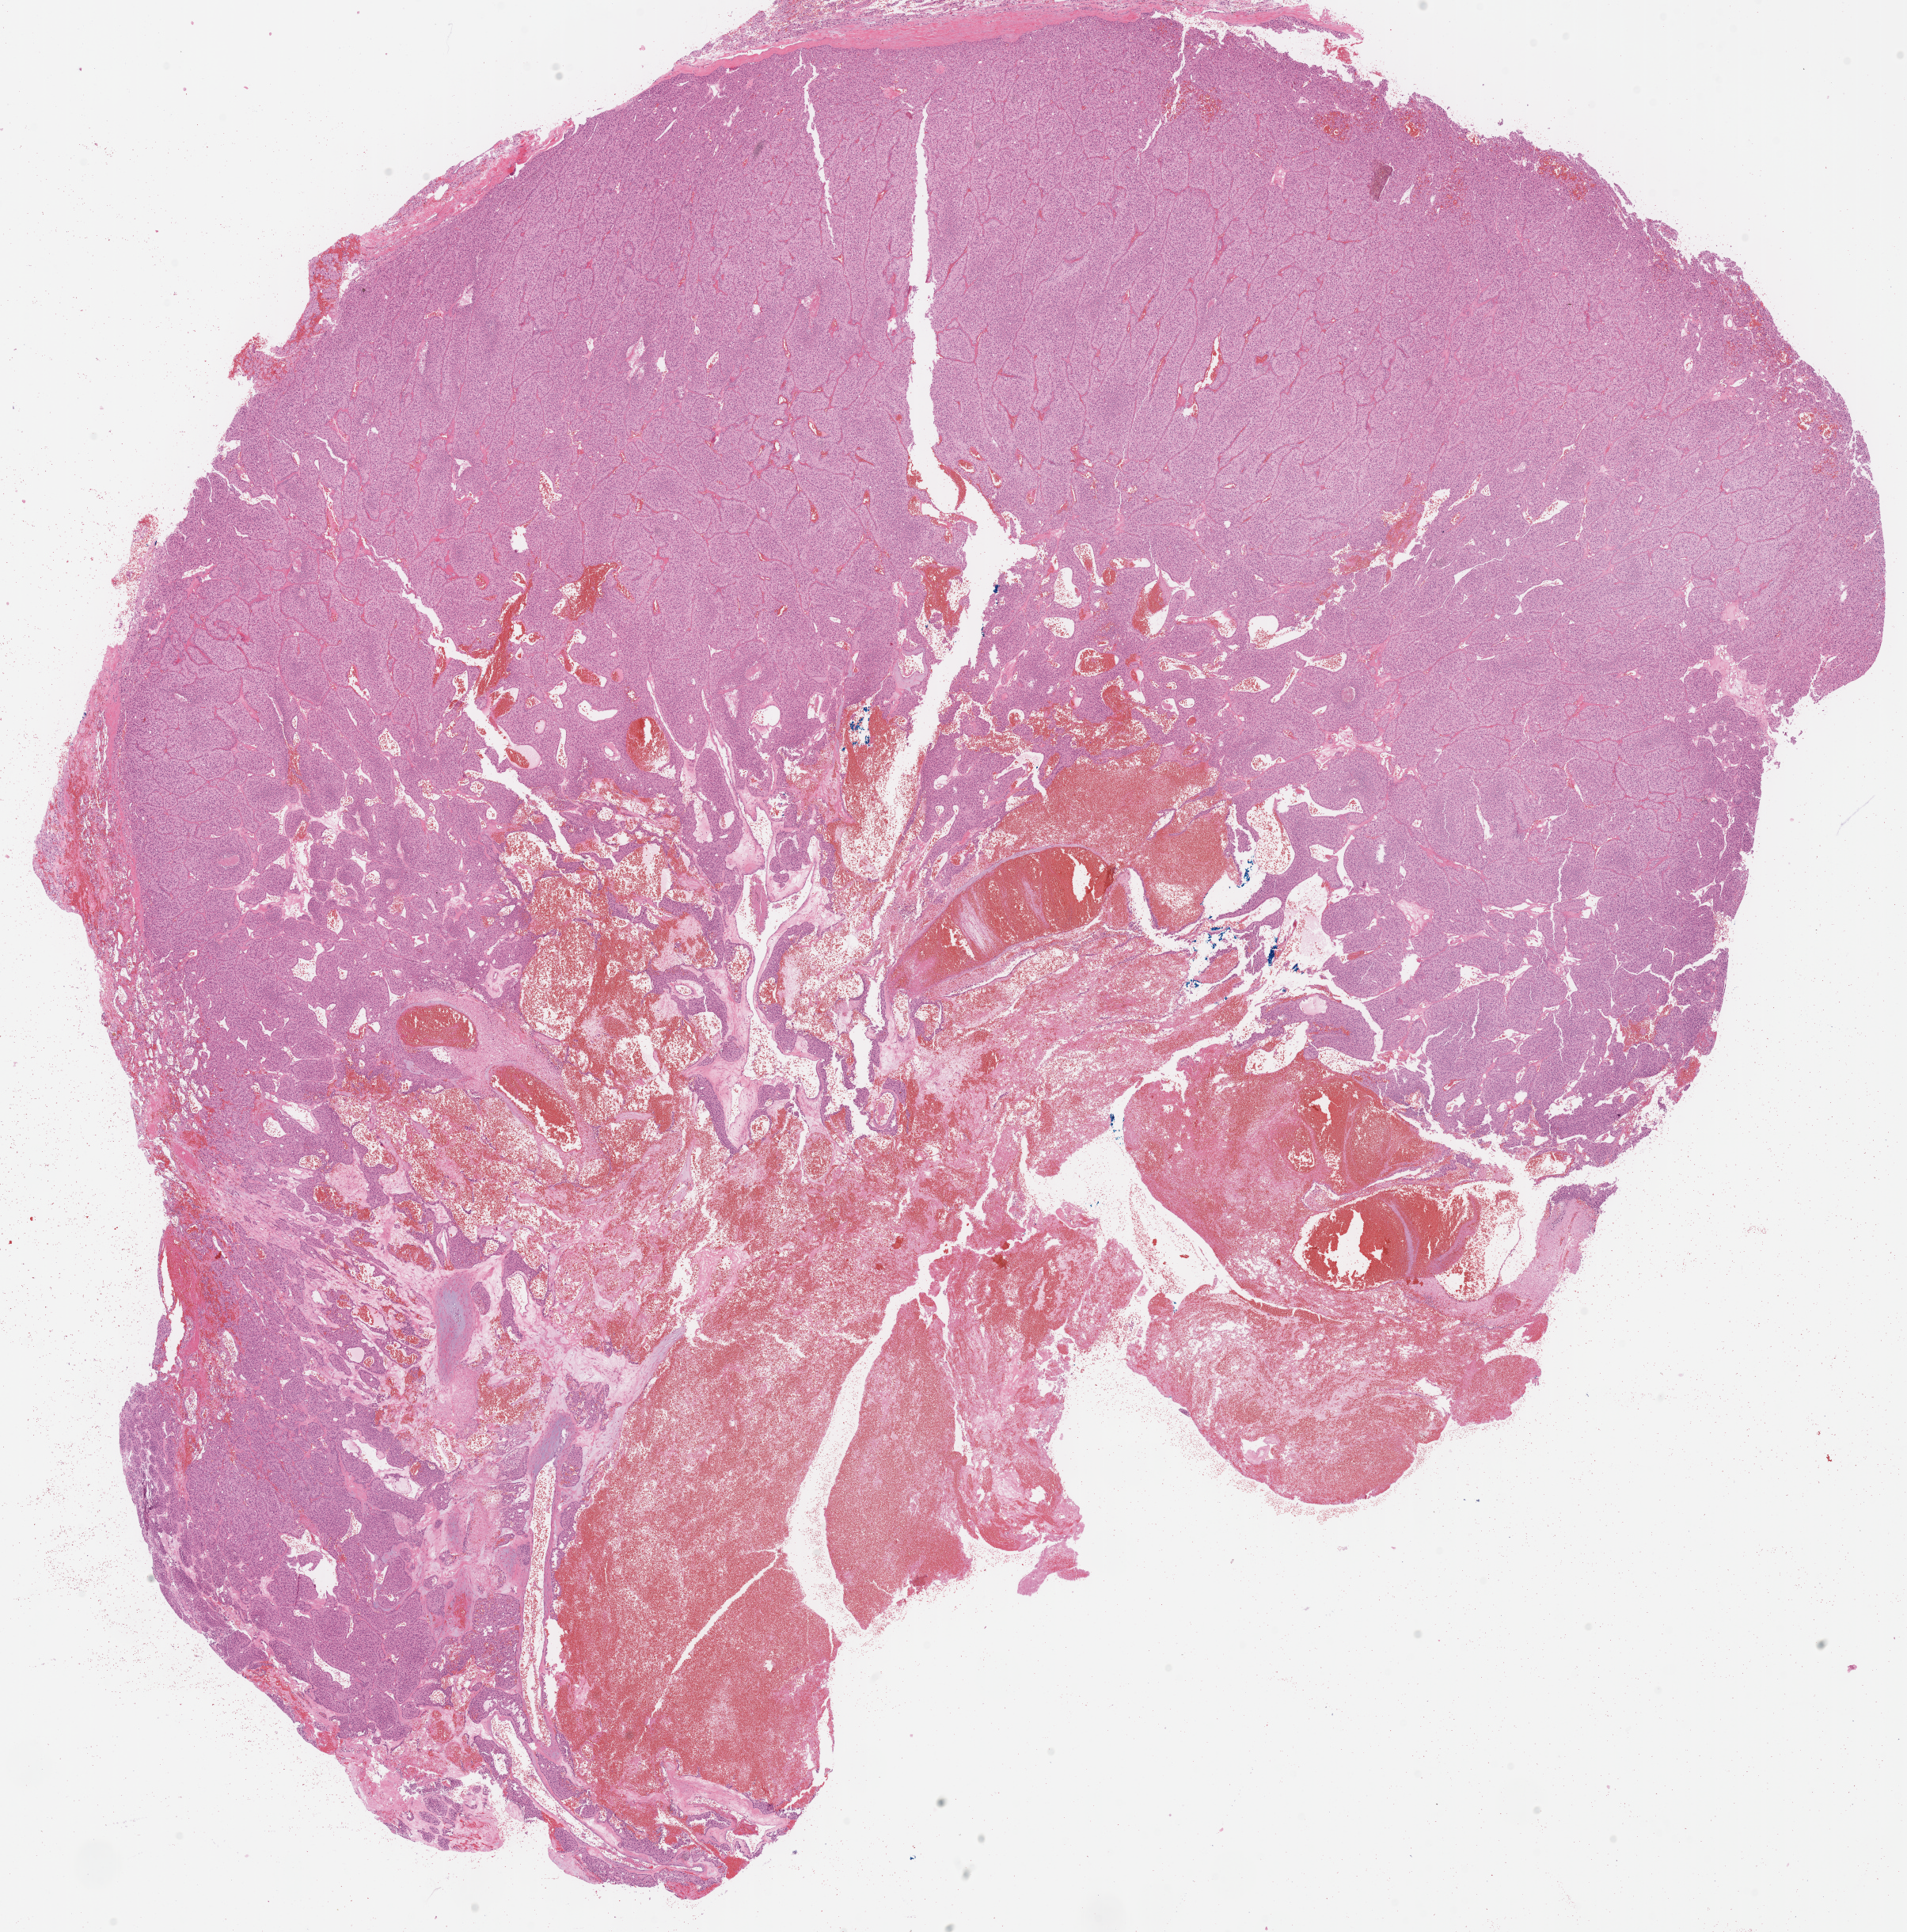
H&E-stained whole-slide image — a low-resolution overview of the entire scanned area, about 19.0 x 19.2 mm (slide scanned at 40x); FFPE section; primary tumour sample from the kidney. Male, age 79 years at initial diagnosis. Histologic grade: G2 (moderately differentiated).
Laterality: left. AJCC pathologic stage: I. Histologic diagnosis: Clear cell adenocarcinoma, NOS. TNM: T1b N0 M0.